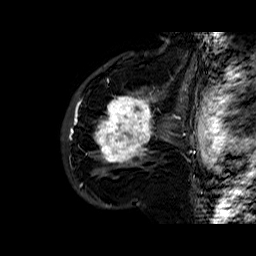
Breast MRI (dynamic contrast-enhanced), one sagittal slice. Slice 42 of 60 in the series (ordered by position). Dynamic contrast-enhanced series, time point 2 of 6 at this slice position (early post-contrast). 1.5 T. TE 6.4 ms, TR 32.8 ms. 4 mm slice thickness. 256 × 256 image matrix, field of view 200 × 200 mm. Female patient. From the clinical record (not read from this slice): setting: breast cancer imaged before/during neoadjuvant chemotherapy; receptor status: HR-positive, HER2-negative.
Structures marked on this image (semi-automatically segmented with operator editing):
- analysis volume of interest (the breast-tissue region the enhancement analysis was run in; not a lesion): bounding box (x1, y1, x2, y2) in pixels: (86, 77, 163, 177)
- tumour enhancement mask (voxels above the 100 % enhancement threshold inside the analysis volume of interest): (94, 92, 156, 165)